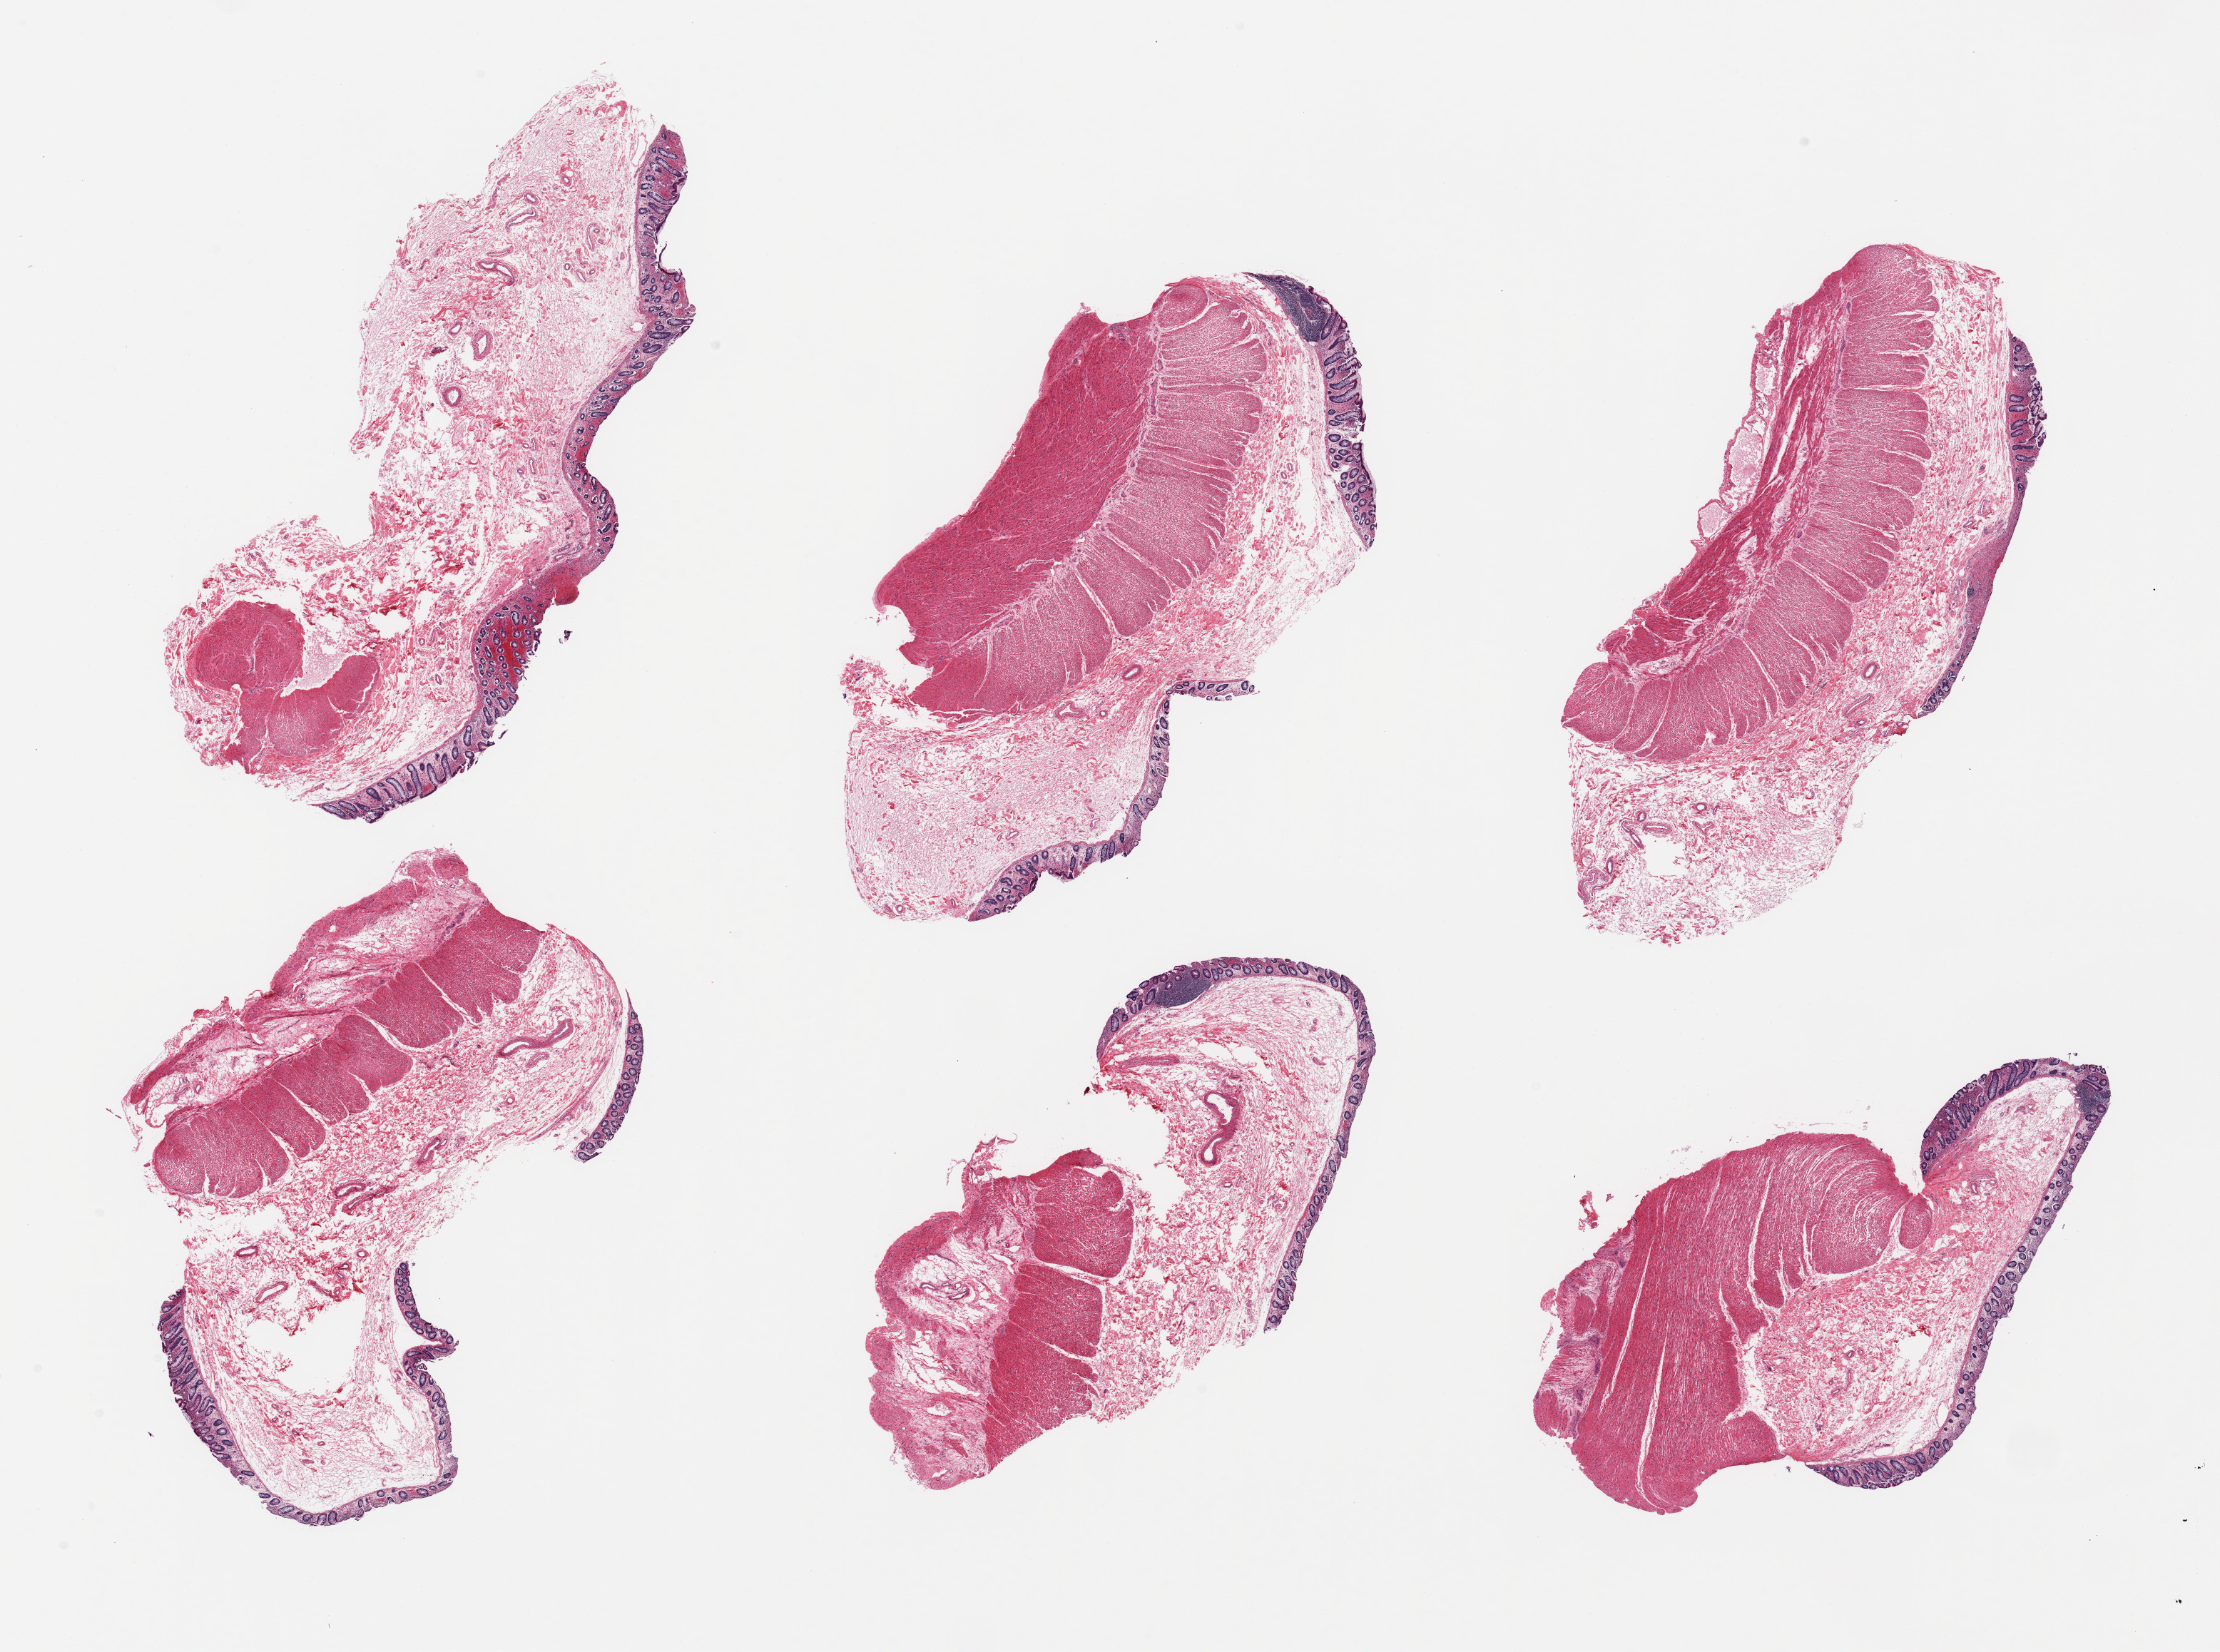
Digitized hematoxylin and eosin (H&E)-stained section, a low-resolution overview of the entire scanned area, about 24.6 x 18.3 mm (from a 20x scan). PAXgene-fixed paraffin-embedded (PFPE) section. Sampled site (target tissue): transverse colon. Tissue donor sample.
* reviewer comment on this tissue sample: 6 pieces; focally moderate autolysis; superficial multifocal mucosal fresh hemorrhage